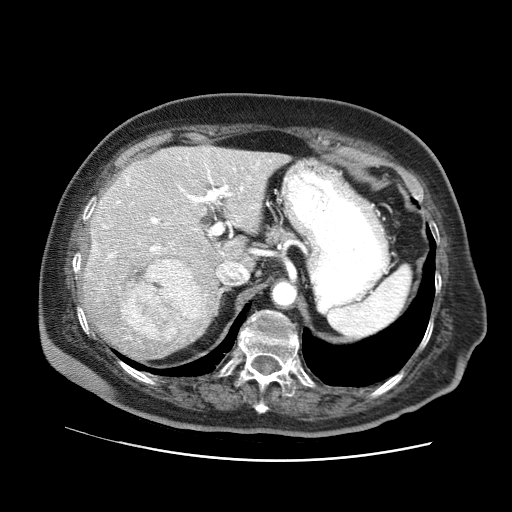
Contrast-enhanced abdominal CT (liver protocol), one axial slice. Position 45 of 73 along the scan axis. 120 kVp. Soft-tissue window (W 400 / L 40 HU). 512 × 512 image matrix, field of view 380 × 380 mm. Case-level facts recorded for this patient, not image findings: diagnosis: hepatocellular carcinoma (patient treated with transarterial chemoembolisation; whether this scan precedes or follows treatment is not stated here); TNM stage (as recorded): Stage-I; Child-Pugh class: A; tumour nodularity: uninodular.
Outlined on this slice (semi-automatic segmentation, software-assisted and operator-edited):
- liver parenchyma outside the tumour (the mass and vessels are separate outlines, so this box may not span the whole liver): bounding box <79,146,288,363> (left, top, right, bottom; pixels)
- mass: <120,259,203,341>
- liver vessels: <103,163,259,258>